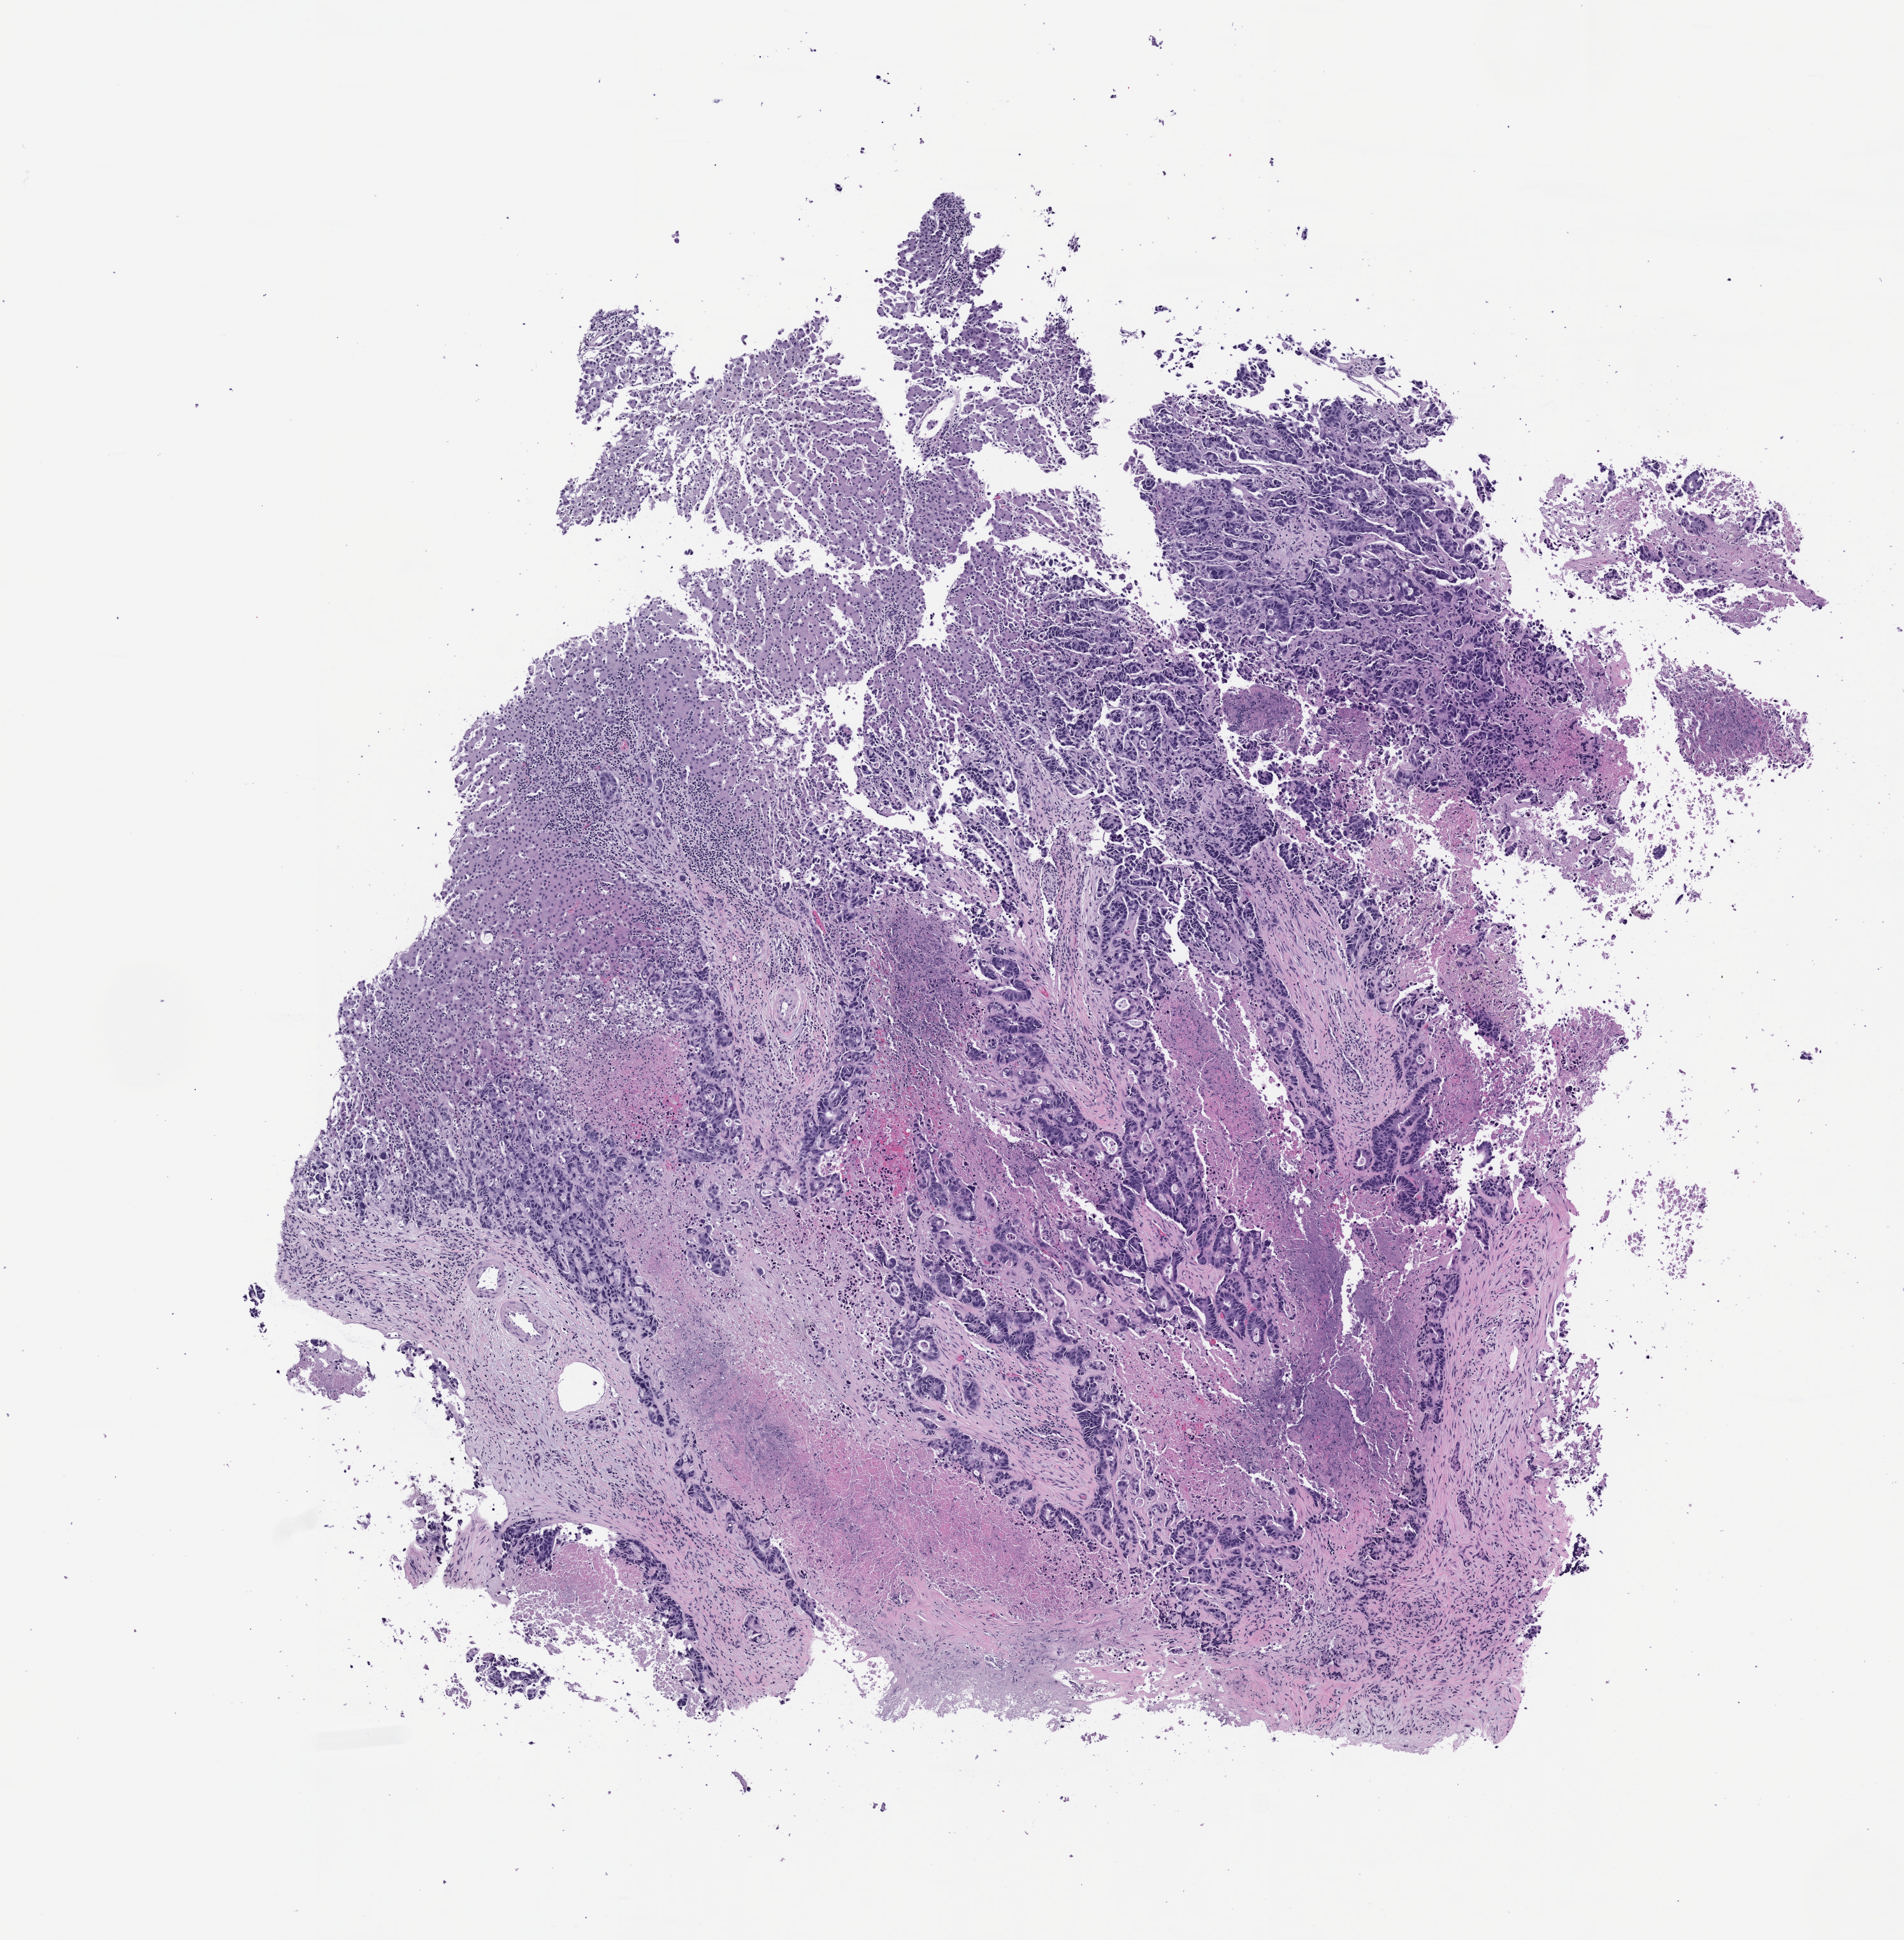
Digitized H&E-stained section of the patient's (originator) tumor tissue — a low-resolution overview of the entire scanned area, about 6.0 x 6.1 mm; FFPE section; tumor site category: rectum. Male patient.
Diagnosis: Rectal Adenocarcinoma.